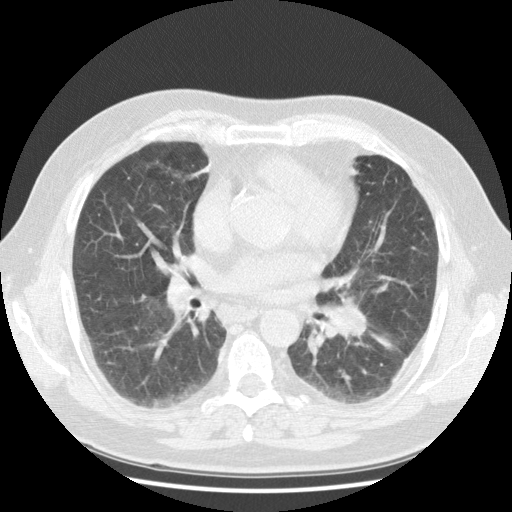
Low-dose screening chest CT, one axial slice; position 59 of 108 along the scan axis; reconstruction kernel STANDARD; 120 kVp; lung window (W 1500 / L -600 HU); 512 × 512 image matrix, field of view 350 × 350 mm.
Structures marked on this image (manually delineated by an expert):
- lesion 1 (tumor, hilum of left lung): bounding box (x1, y1, x2, y2) in pixels: (325, 306, 367, 336)